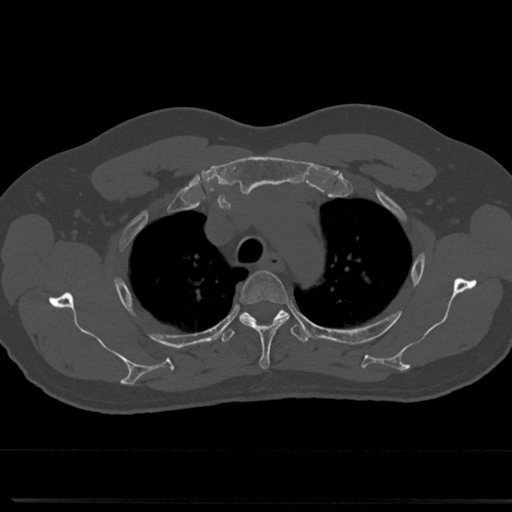
CT including the spine, one axial slice; slice 574 of 817 in the series (ordered by position); reconstruction kernel Br40s/3; bone window (W 1800 / L 400 HU); 0.5 mm slice thickness; 512 × 512 image matrix, field of view 355 × 355 mm. Male patient, age 61 years. From the clinical record (not read from this slice): primary cancer: prostate.
Annotated regions visible in this slice (semi-automatic segmentation, software-assisted and operator-edited):
- T3 vertebra: box from (x=241, y=271) to (x=287, y=369) px
- T4 vertebra: (x=220, y=301)–(x=310, y=345)